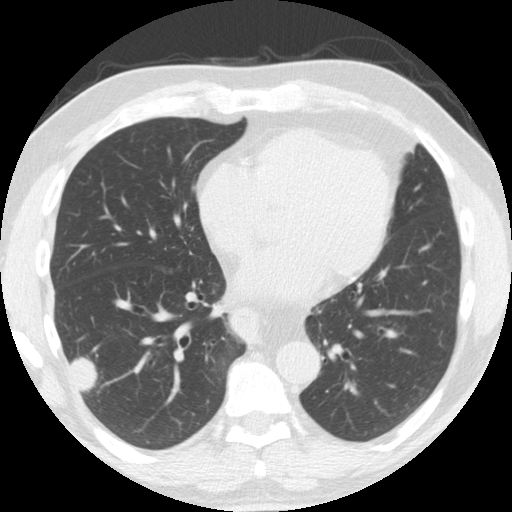
Low-dose screening chest CT, one axial slice; slice 71 of 174 in the series (ordered by position); reconstruction kernel STANDARD; 120 kVp; lung window (W 1500 / L -600 HU); 512 × 512 image matrix.
Structures marked on this image (manually delineated by an expert):
- lesion 1 (tumor, lower lobe of right lung): bounding box (x1, y1, x2, y2) in pixels: (71, 357, 98, 392)